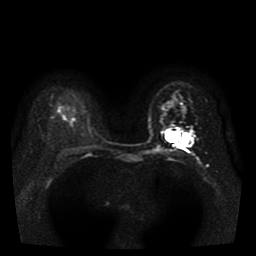
Breast MRI, one axial slice; position 30 of 41 along the scan axis; diffusion-weighted series; image 2 of 4 stored at this slice position (different b-values; order by instance number); 1.5 T; 5 mm slice thickness; 256 × 256 image matrix. Female patient.
Annotated regions visible in this slice (manually delineated by an expert):
- tumour on diffusion-weighted imaging: bounding box (x1, y1, x2, y2) in pixels: (177, 137, 187, 145)